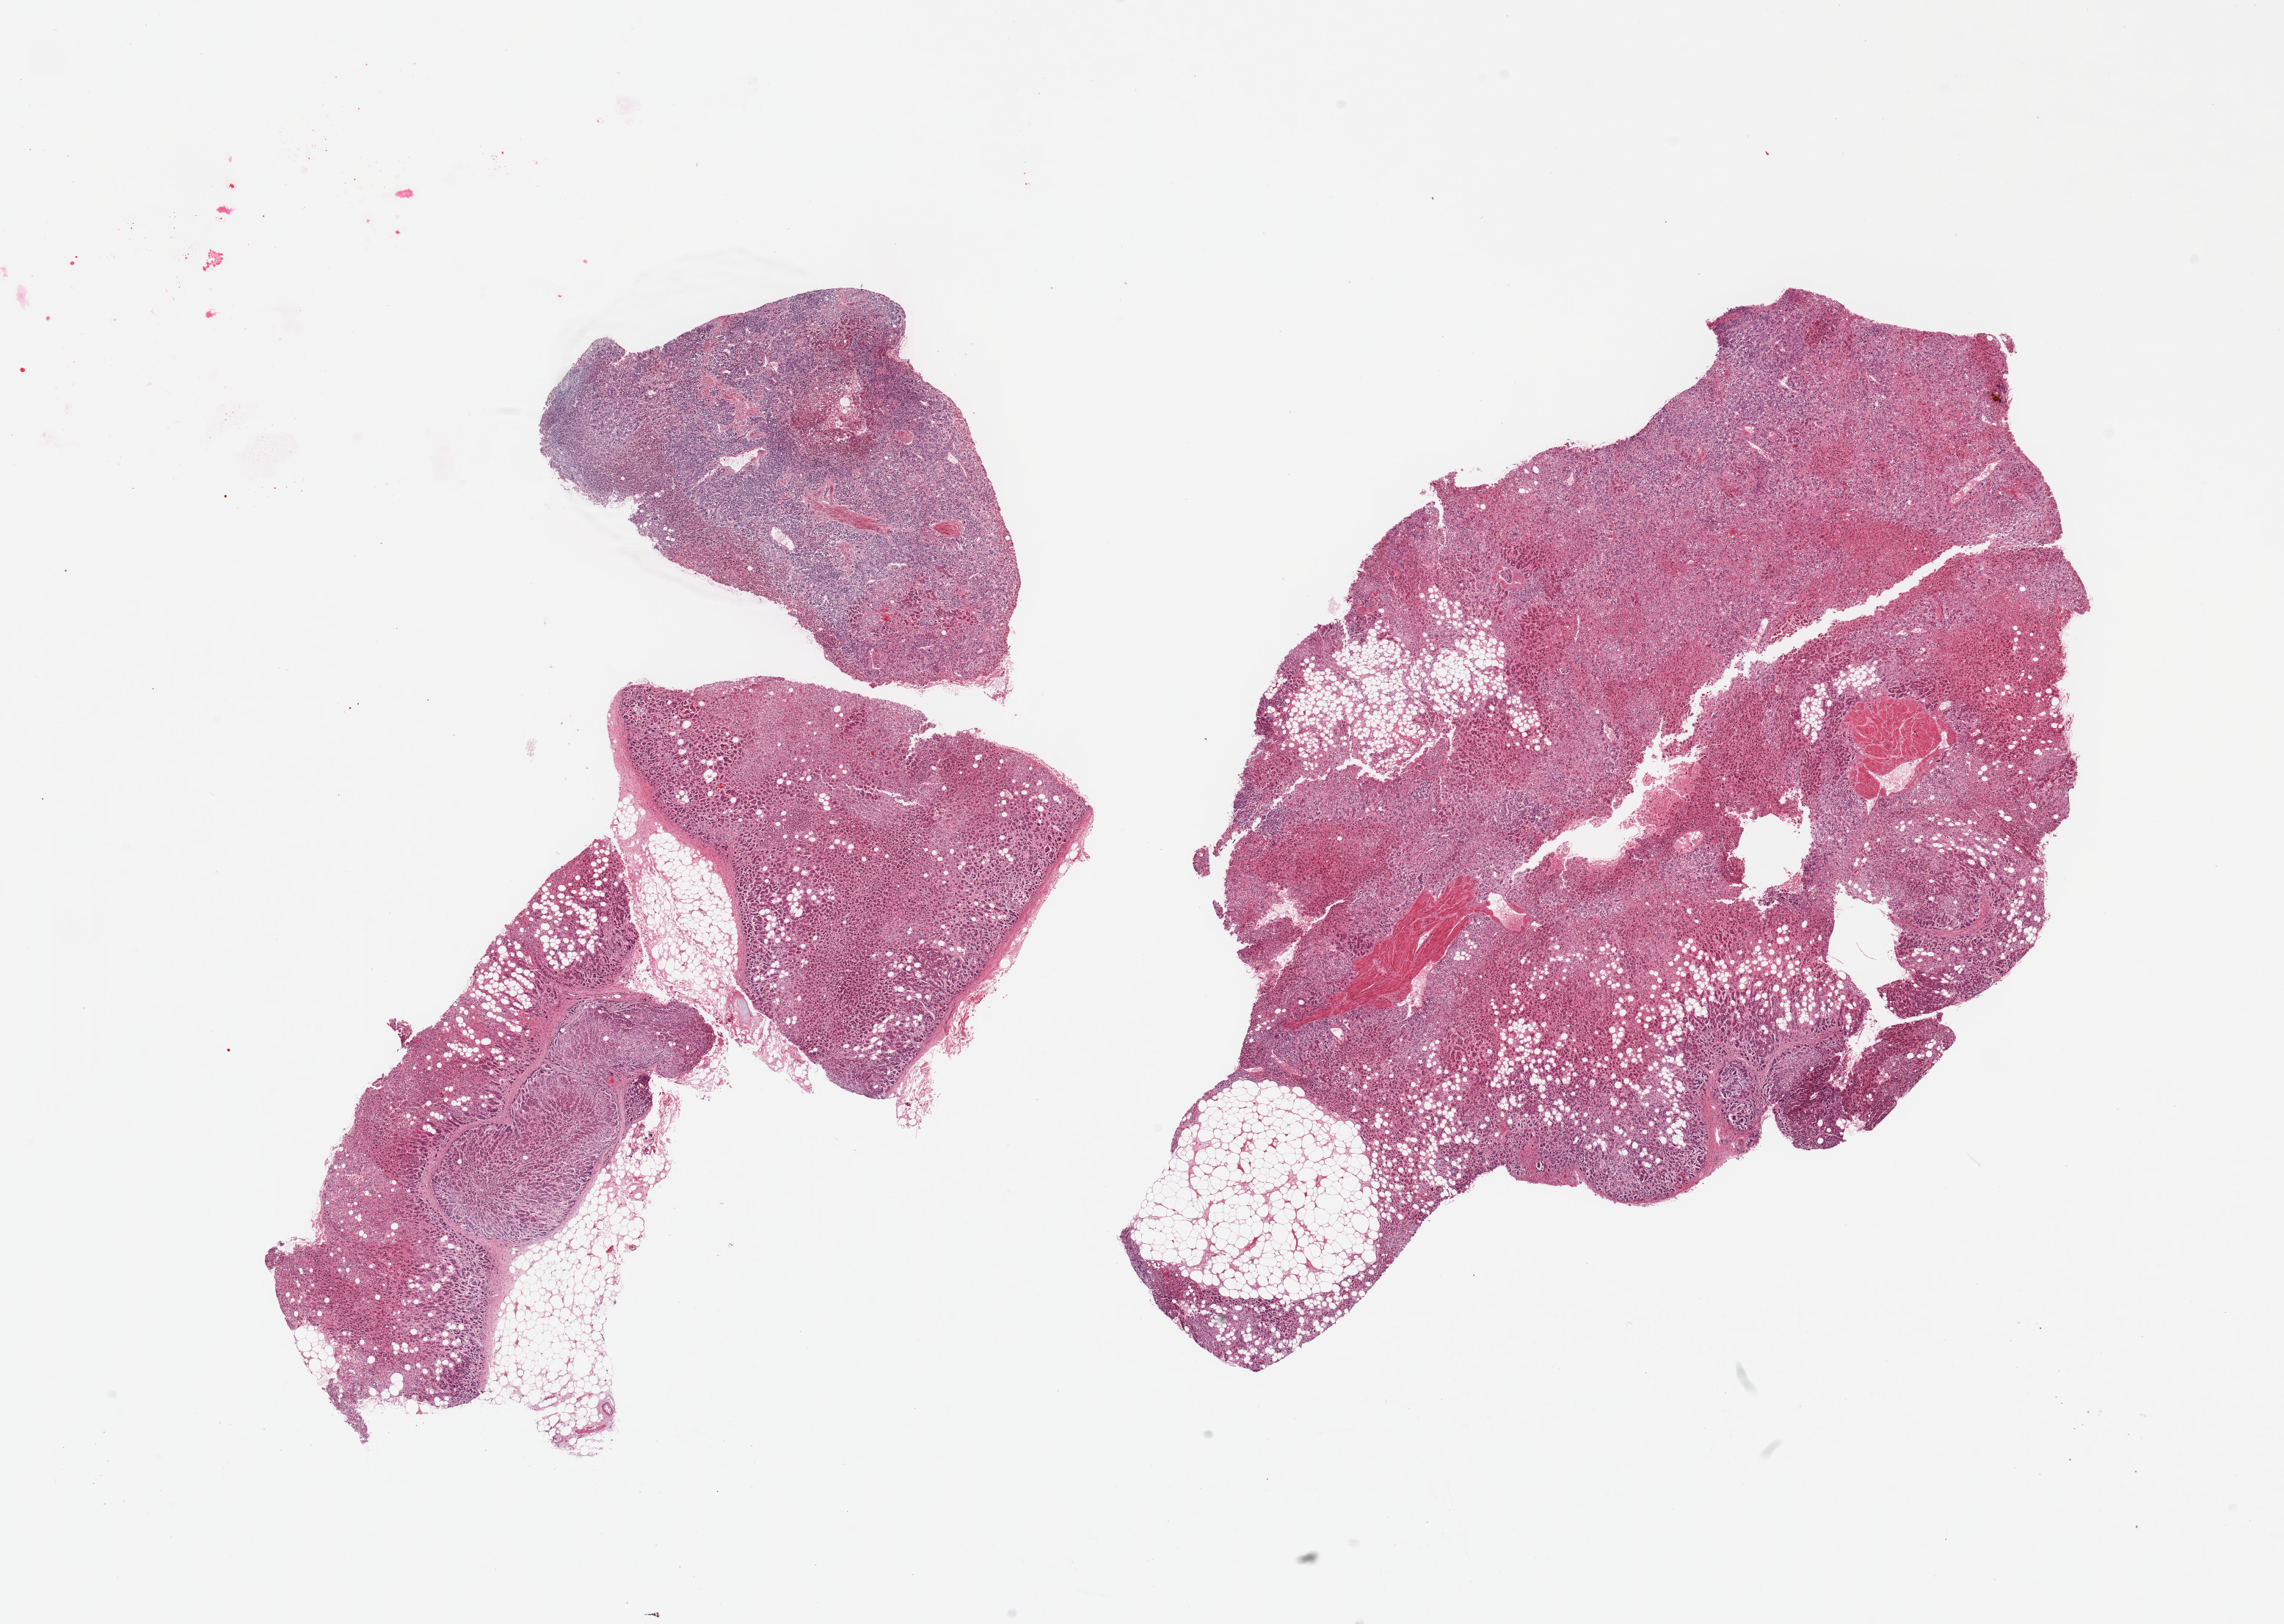
Digitized haematoxylin and eosin-stained section, shown as a low-resolution overview of the whole scanned area (about 24.6 x 17.5 mm), PAXgene-fixed, paraffin-embedded tissue, section of adrenal gland (target tissue), donor tissue sample.
• pathologist's review note for this sample: 3 pieces; moderately autolyzed adrenal cortex with fatty degeneration and ~20% internal and external fat; two smooth muscle fragments